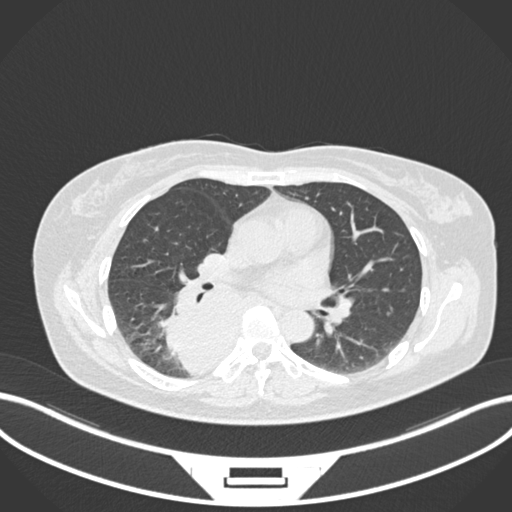
Chest CT, one axial slice; position 593 of 677 along the scan axis; lung window (W 1500 / L -600 HU); 1 mm slice thickness; 512 × 512 image matrix. Female patient, age 54 years. From the clinical record (not read from this slice): clinical TNM (as recorded): T4 N0 M0.
Annotated regions visible in this slice (rectangle marked by the reading radiologist):
- lung tumour (recorded histology: adenocarcinoma): box from (x=156, y=280) to (x=243, y=381) px